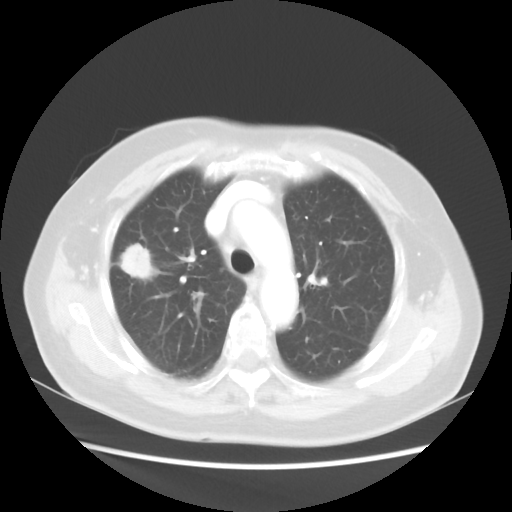
Chest CT, one axial slice. Reconstruction kernel STANDARD. 100 kVp. Lung window (W 1500 / L -600 HU). 5 mm slice thickness. 512 × 512 image matrix. Female patient, age 75 years. Case-level facts recorded for this patient, not image findings: clinical TNM (as recorded): T1c N0 M0.
Outlined on this slice (bounding box drawn by a radiologist):
- lung tumour (recorded histology: adenocarcinoma): bounding box (x1, y1, x2, y2) in pixels: (113, 237, 155, 286)